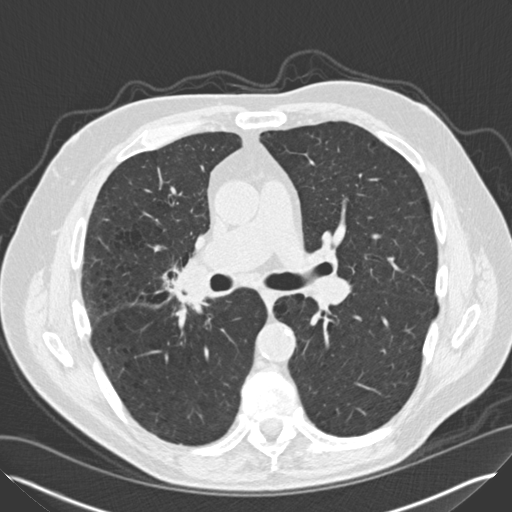
Low-dose screening chest CT, axial slice. Second annual screen. Lung window (W 1500 / L -600 HU). Standard (soft-tissue) reconstruction kernel (B30f). 120 kVp. 512 × 512 image matrix, field of view 370 × 370 mm. Male participant, aged 65 years at enrolment. Current smoker at enrolment.
- Expert reader's lesion annotation, bounding box [x1, y1, x2, y2] px = [155, 263, 213, 315].
- Reader record for this screening exam (exam-level; its link to the box is not recorded): non-calcified nodule or mass ≥4 mm, left lower lobe, 12 × 8 mm, smooth margins, soft tissue attenuation, pre-existing on the prior screen: yes; interval growth: yes.
- Note: the box lies in the patient's right hemithorax on this image, whereas the reader's record names the left lung; they may be different findings.
- Later outcome: lung cancer diagnosed 67 days after this screen — non-small cell carcinoma, left lower lobe, right hilum, poorly differentiated (G3), stage IV (AJCC 6th edition), 5 mm at pathology.